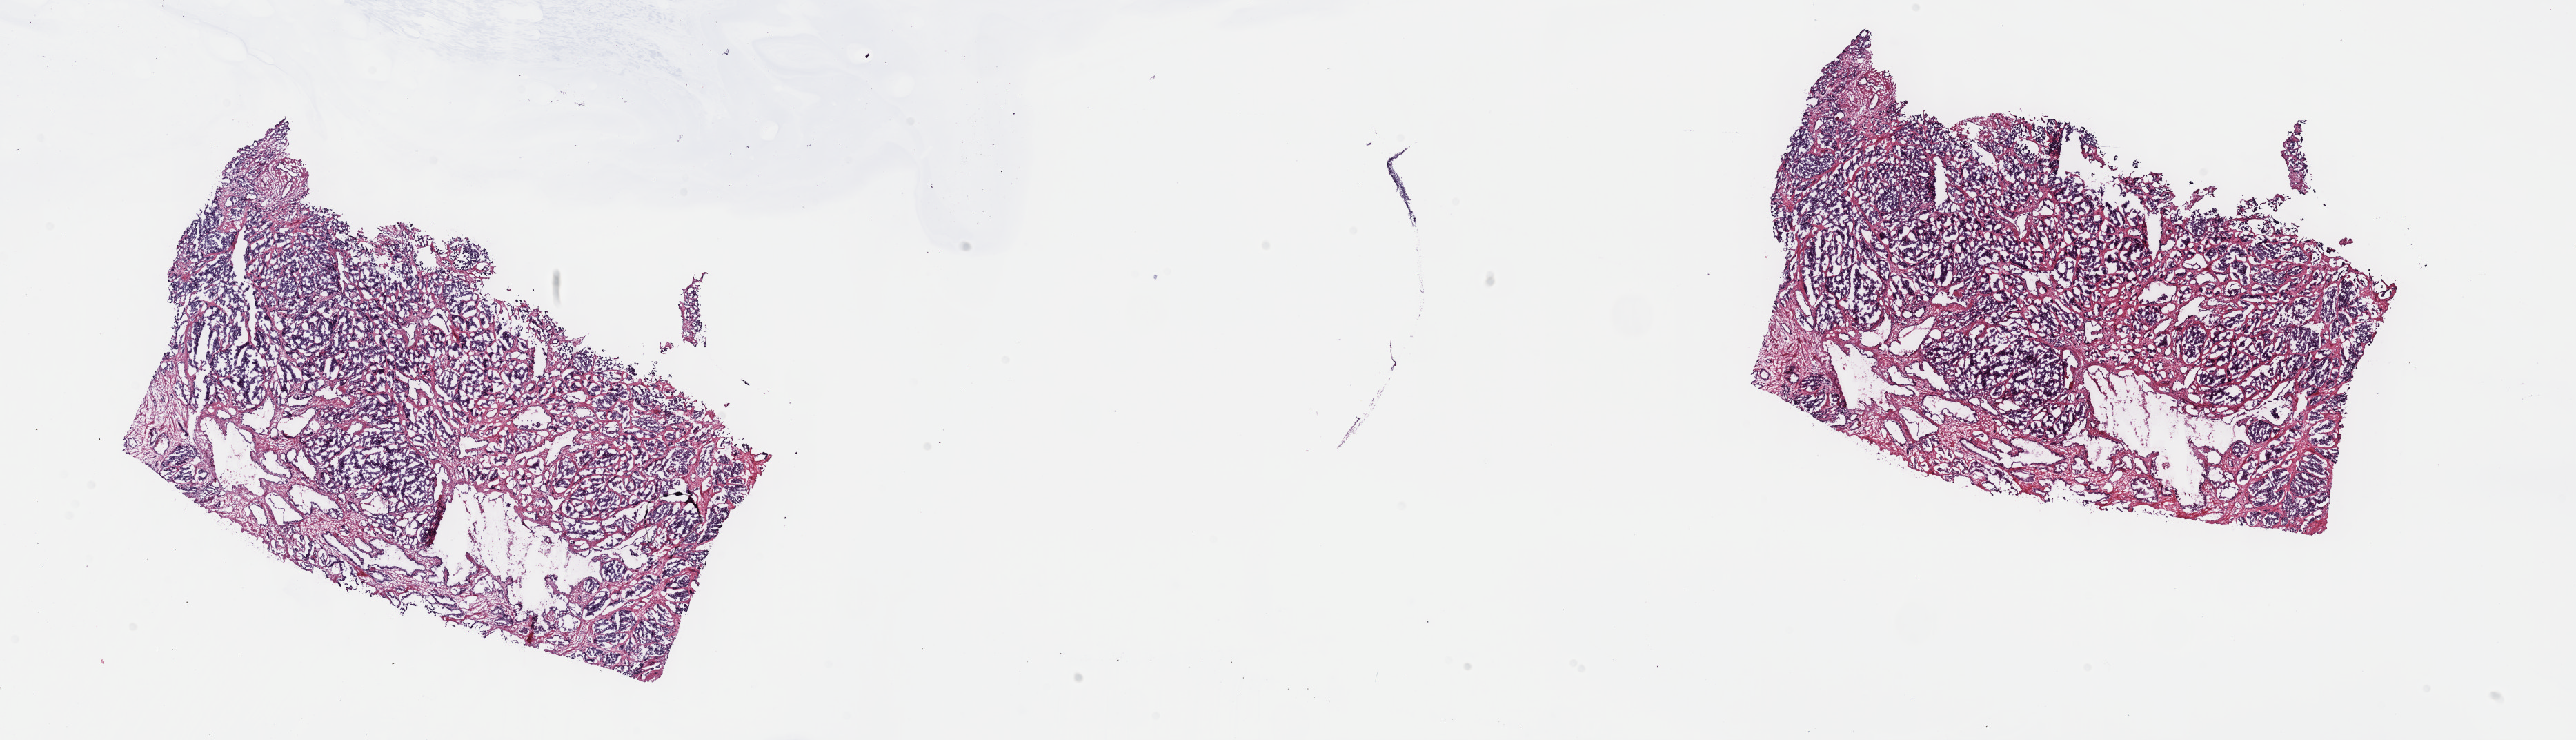
Whole-slide histology image, Hematoxylin and eosin (H&E) stained, a low-resolution overview of the entire scanned area, about 30.2 x 8.7 mm, frozen section from the top of the tissue portion, prostate, primary tumour sample. Male patient; age at initial diagnosis 62 years. Gleason score: 8 (4+4). Slide review estimates, as recorded: tumour cells 49%, tumour nuclei 90%, normal cells 1%, stromal cells 47%, necrosis 3%. Inflammatory infiltration, as recorded: lymphocyte infiltration 4%, monocyte infiltration 0%, neutrophil infiltration 0%.
Pathologic diagnosis: Adenocarcinoma, NOS (prostate gland). Lymph nodes positive (case pathology): 4 of 10 examined.